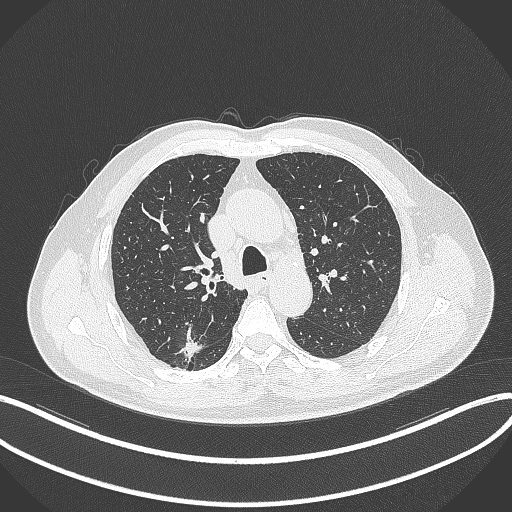
Chest CT, one axial slice; slice 257 of 359 in the series (ordered by position); 120 kVp; lung window (W 1500 / L -600 HU); 512 × 512 image matrix. Male patient, age 69 years. From the clinical record (not read from this slice): clinical TNM (as recorded): T1b N0 M0; histopathological grade: G2-3.
Outlined on this slice (bounding box drawn by a radiologist):
- lung tumour (recorded histology: adenocarcinoma): bounding box <172,328,207,366> (left, top, right, bottom; pixels)